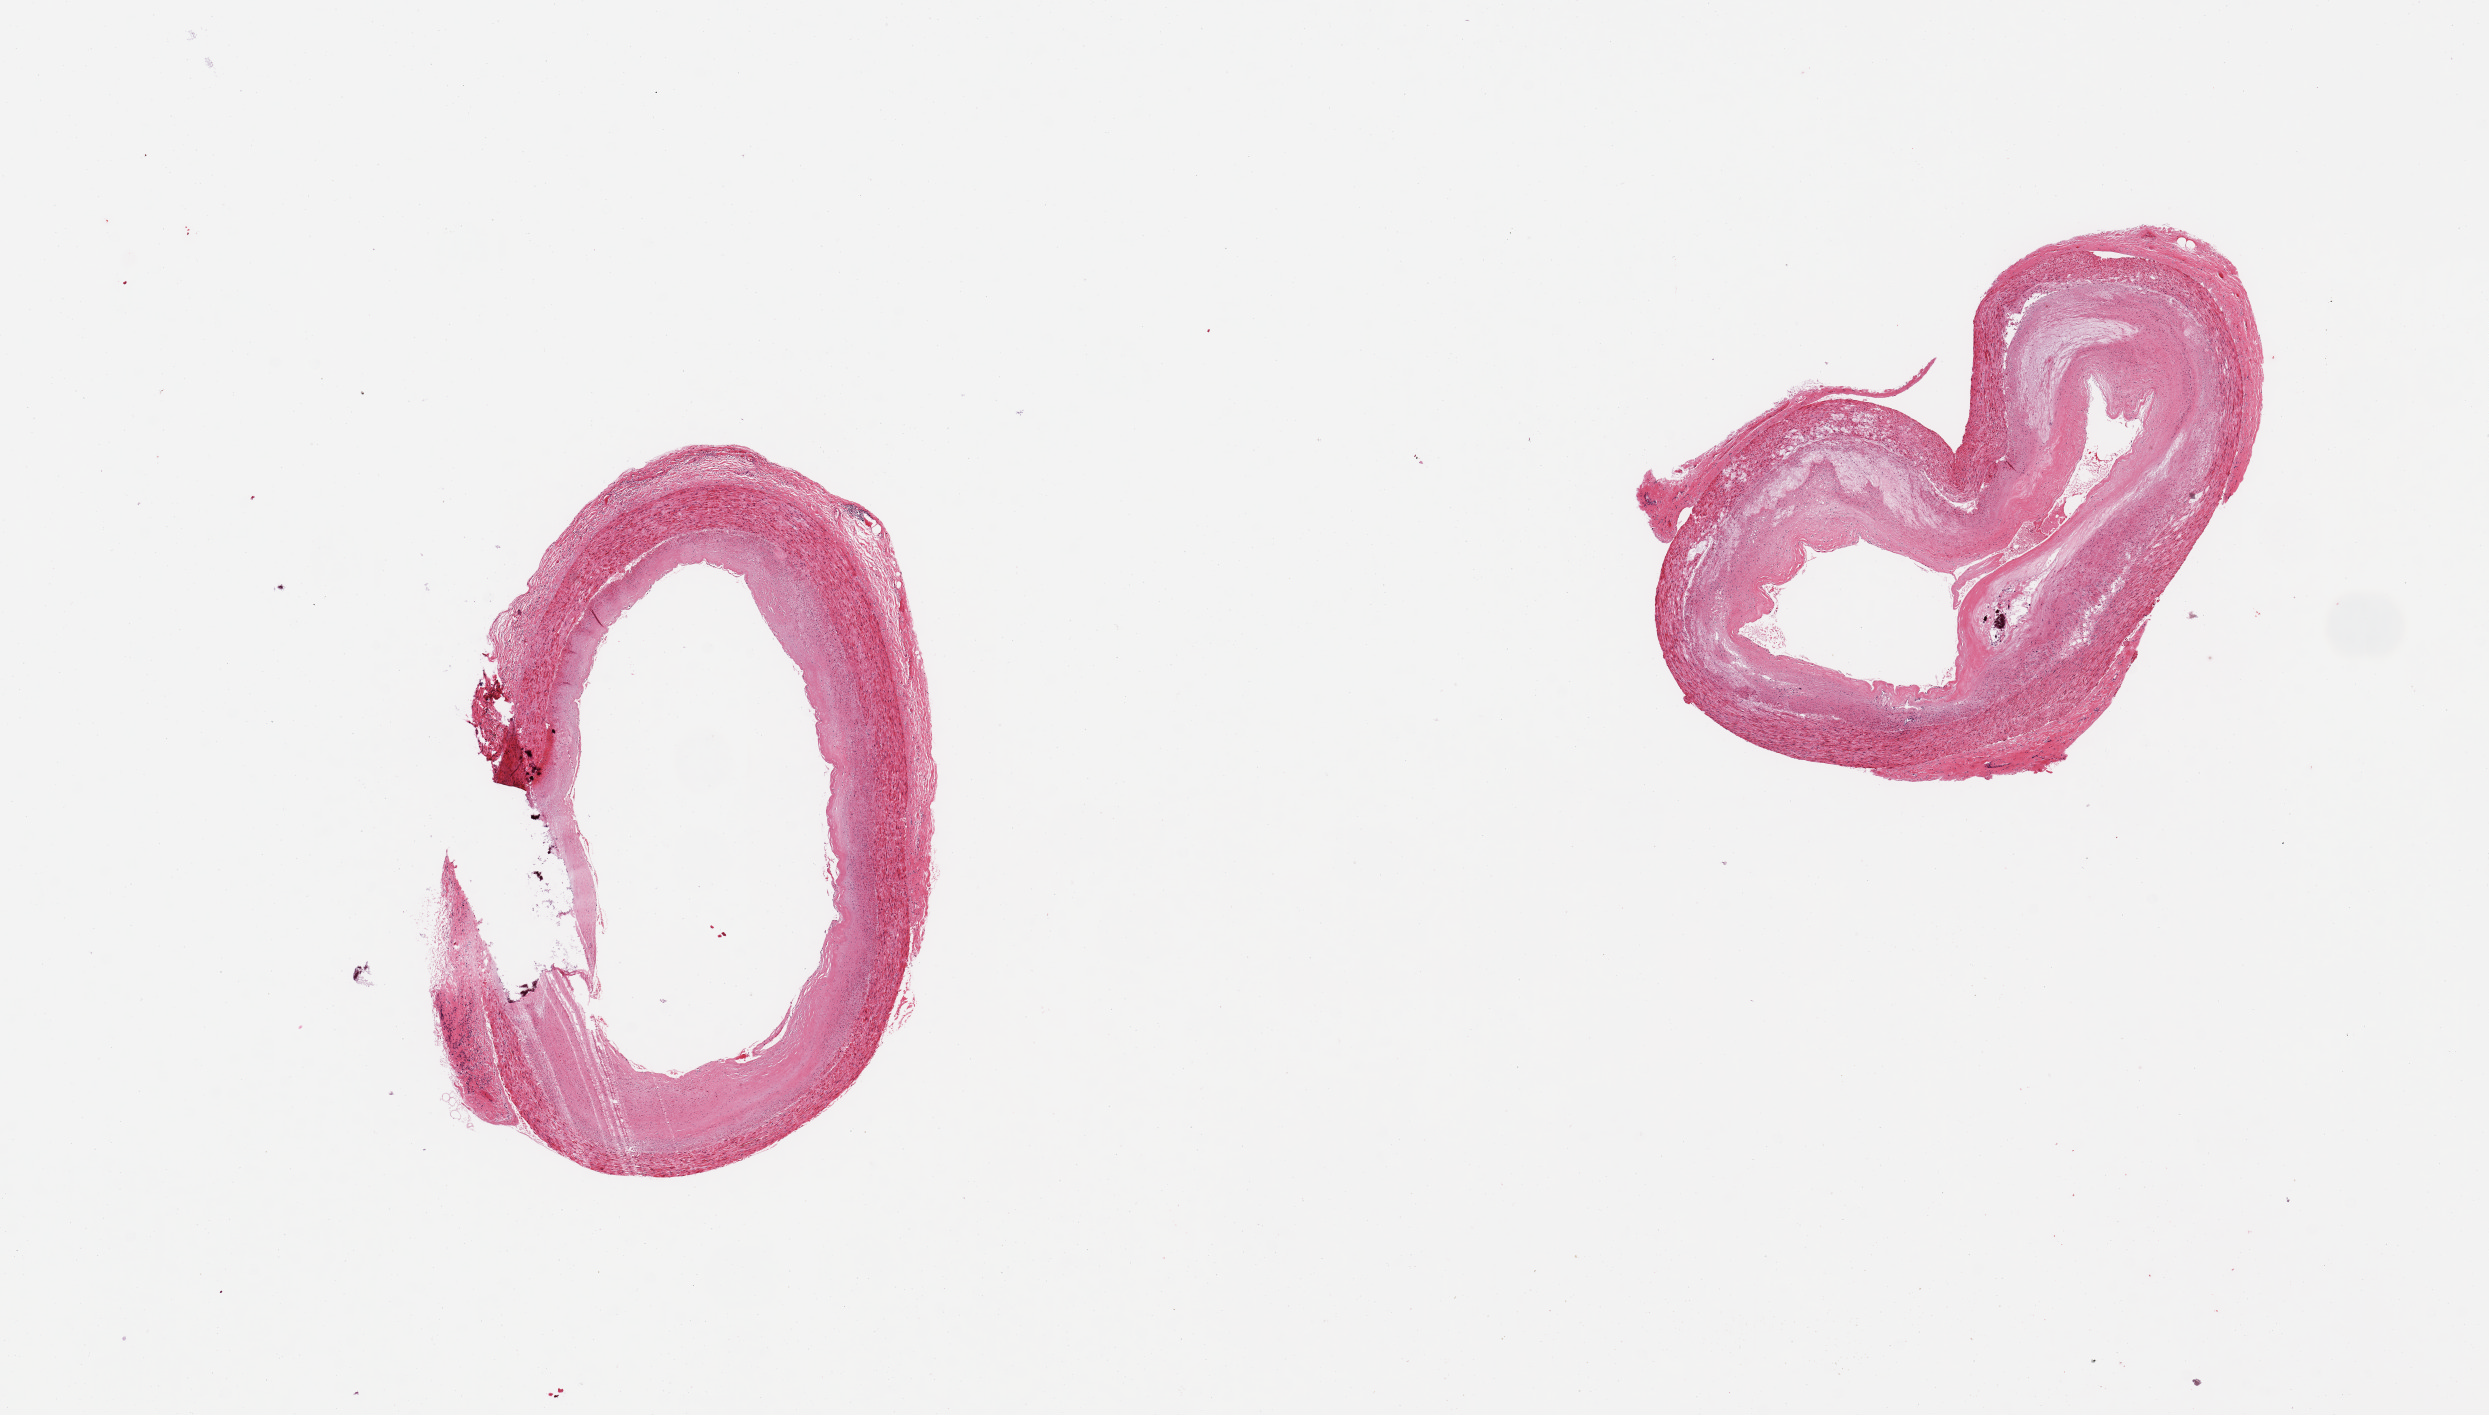
Digitized H&E-stained section, whole scanned area (about 19.7 x 11.2 mm, slide scanned at 20x) shown as a low-resolution overview. PAXgene-fixed, paraffin-embedded tissue. Section of coronary artery (target tissue). Tissue donor sample. Male donor.
Pathologist's review note for this sample: 2 pieces, ~60% obstructive atherosis.